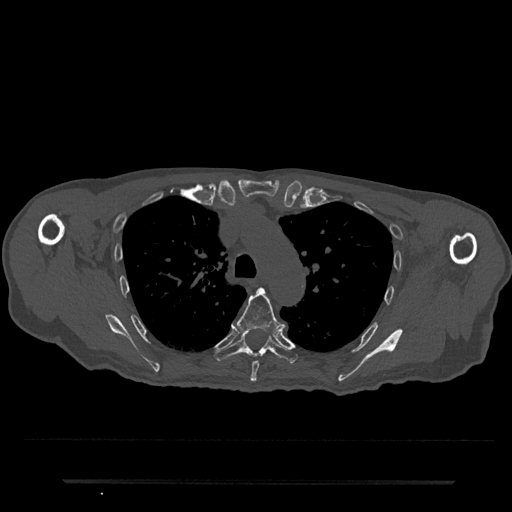
CT including the spine, one axial slice. Slice 557 of 797 in the series (ordered by position). Reconstruction kernel Br40s/3. 120 kVp. Bone window (W 1800 / L 400 HU). 512 × 512 image matrix, field of view 427 × 427 mm. Patient: male, 74 years. Case-level facts recorded for this patient, not image findings: primary cancer: prostate.
Structures marked on this image (semi-automatic segmentation, software-assisted and operator-edited):
- T5 vertebra: bounding box [x1, y1, x2, y2] px = [237, 288, 286, 382]
- T6 vertebra: [214, 332, 298, 364]